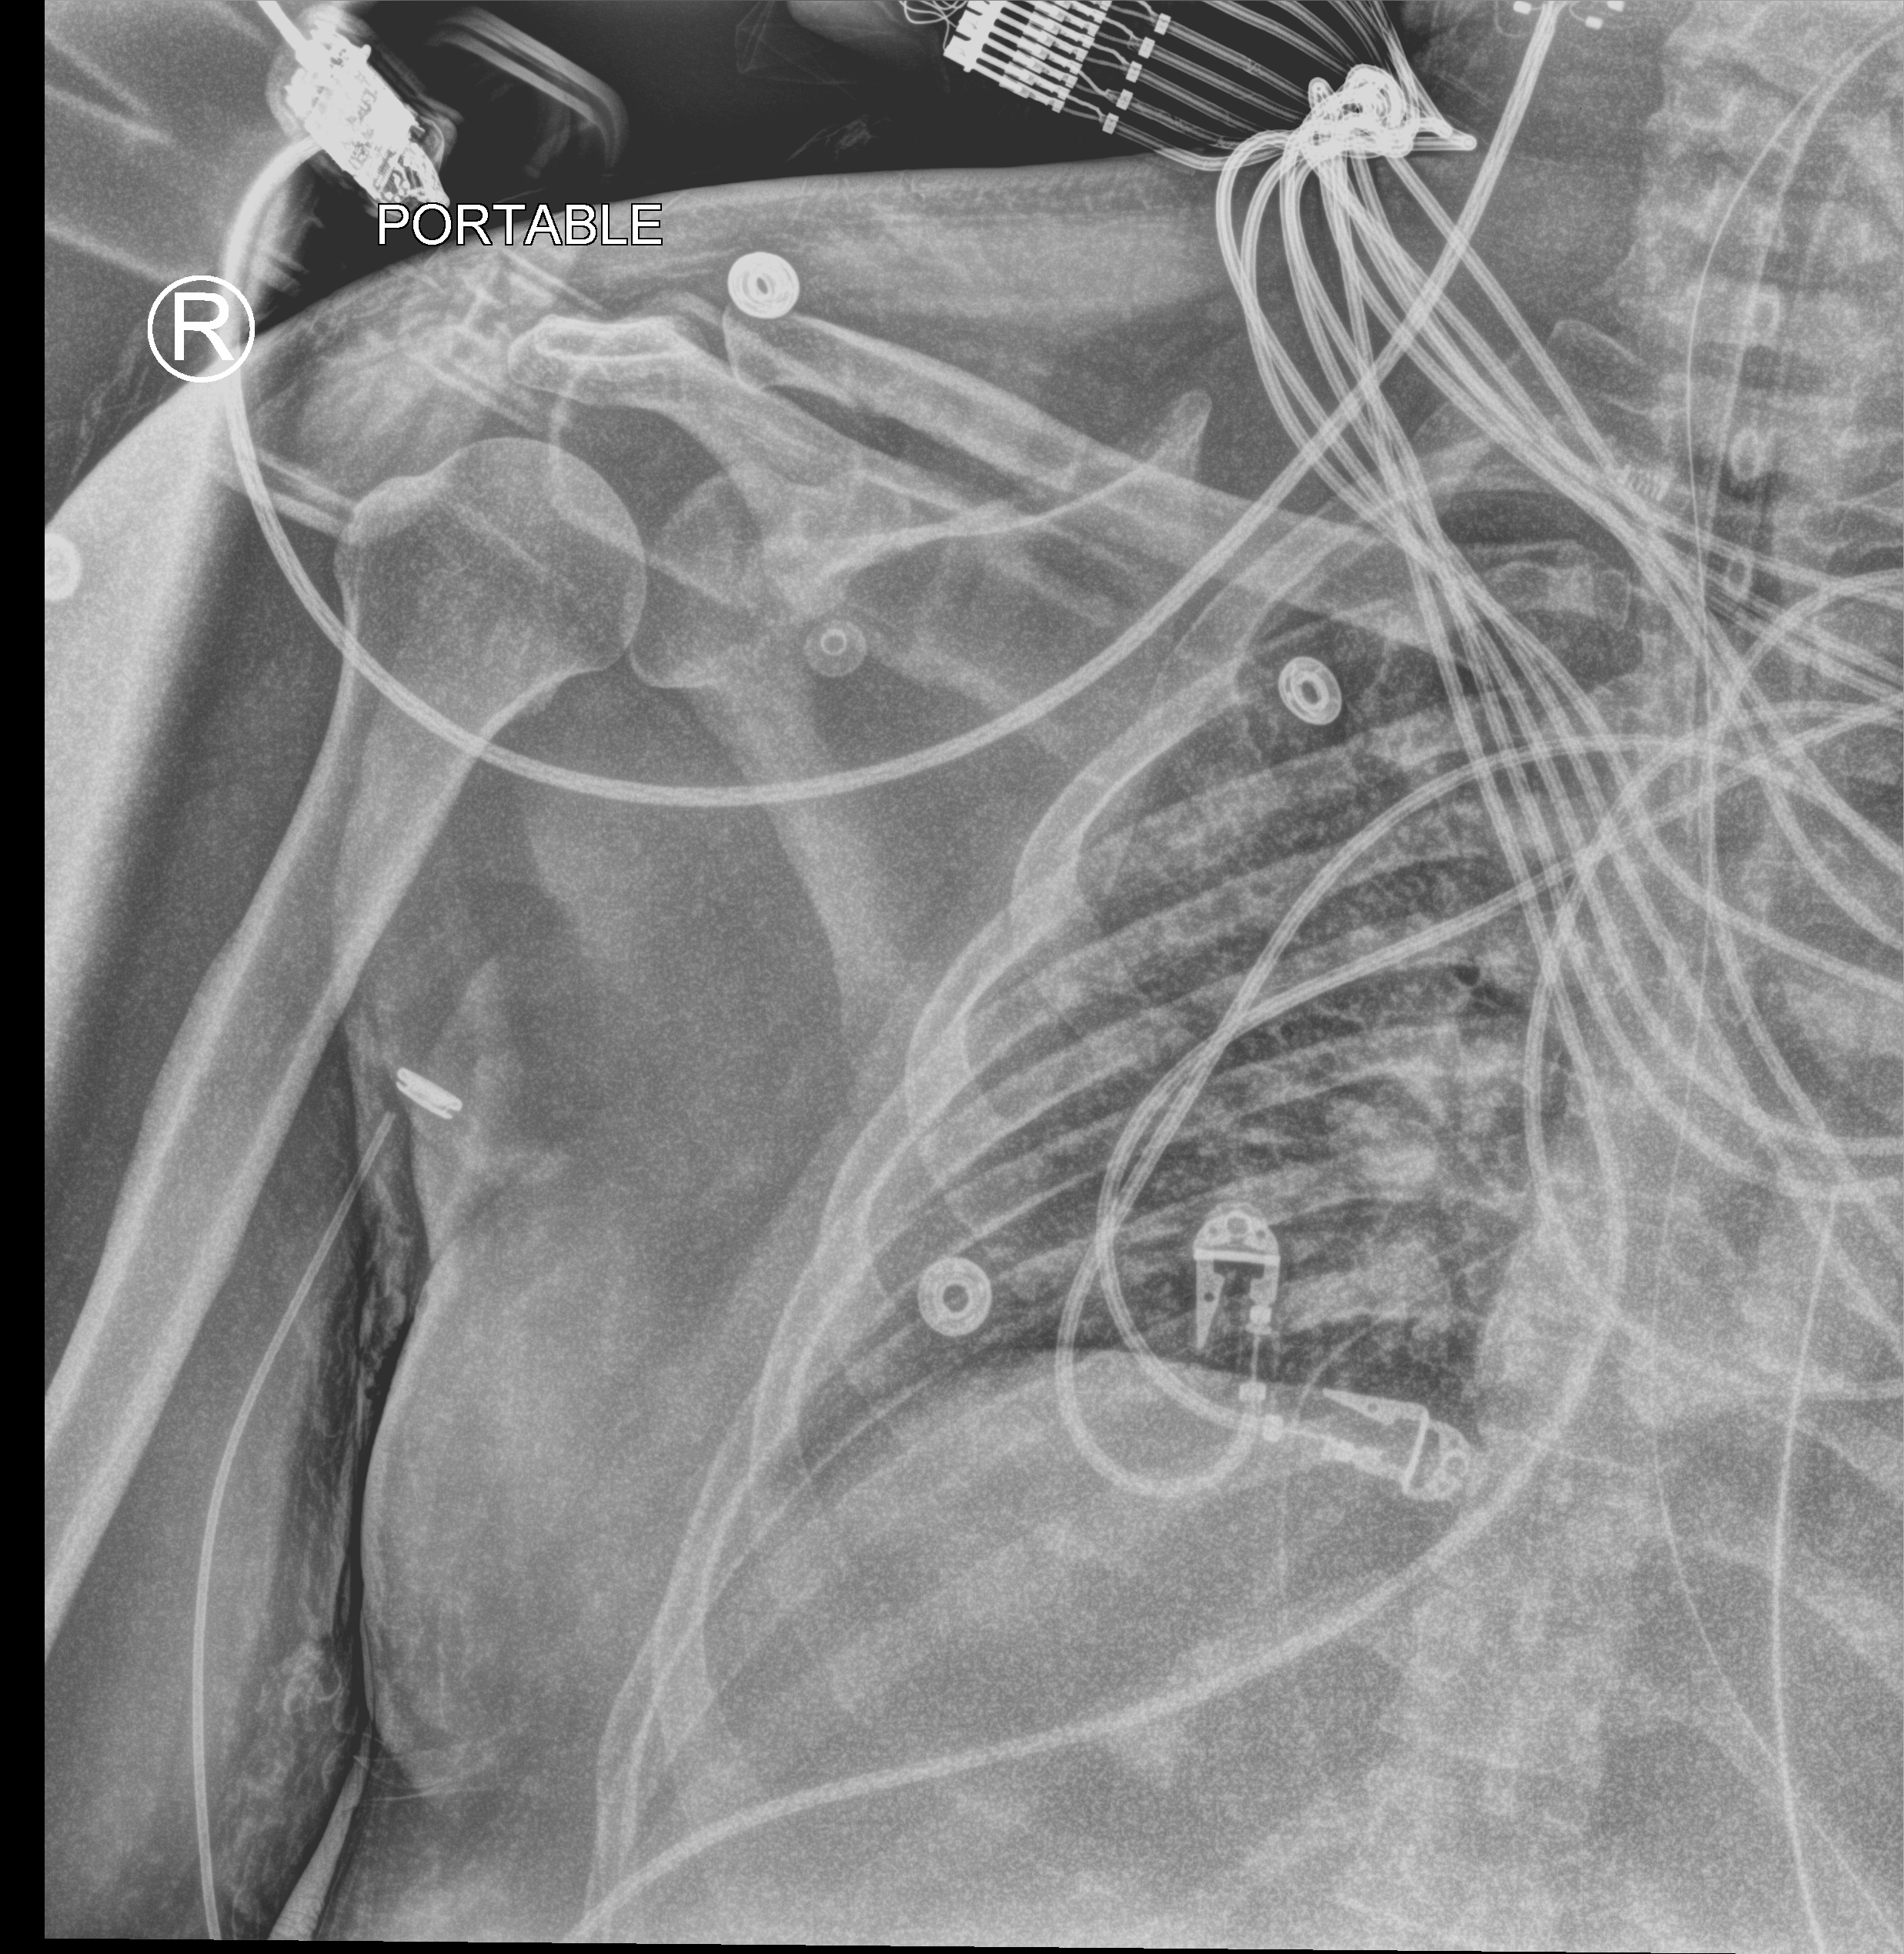
Portable chest radiograph; anteroposterior (AP) projection. Patient hospitalised with COVID-19, aged 18–59 years.
Hospital-stay facts (about this admission, not read from this image; timing relative to this image not recorded):
- length of hospital stay: 19 days